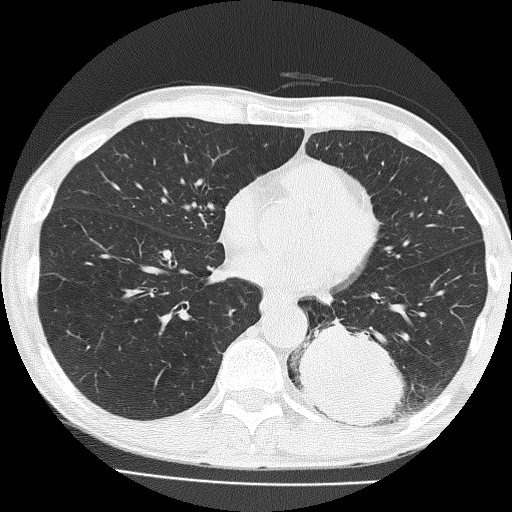
Low-dose screening chest CT, one axial slice. Slice 68 of 160 in the series (ordered by position). Reconstruction kernel FC51. Lung window (W 1500 / L -600 HU). 2 mm slice thickness. 512 × 512 image matrix, field of view 324 × 324 mm.
Annotated regions visible in this slice (outlined manually by an expert reader):
- lesion 1 (tumor, lower lobe of left lung): bounding box (x1, y1, x2, y2) in pixels: (296, 320, 405, 427)